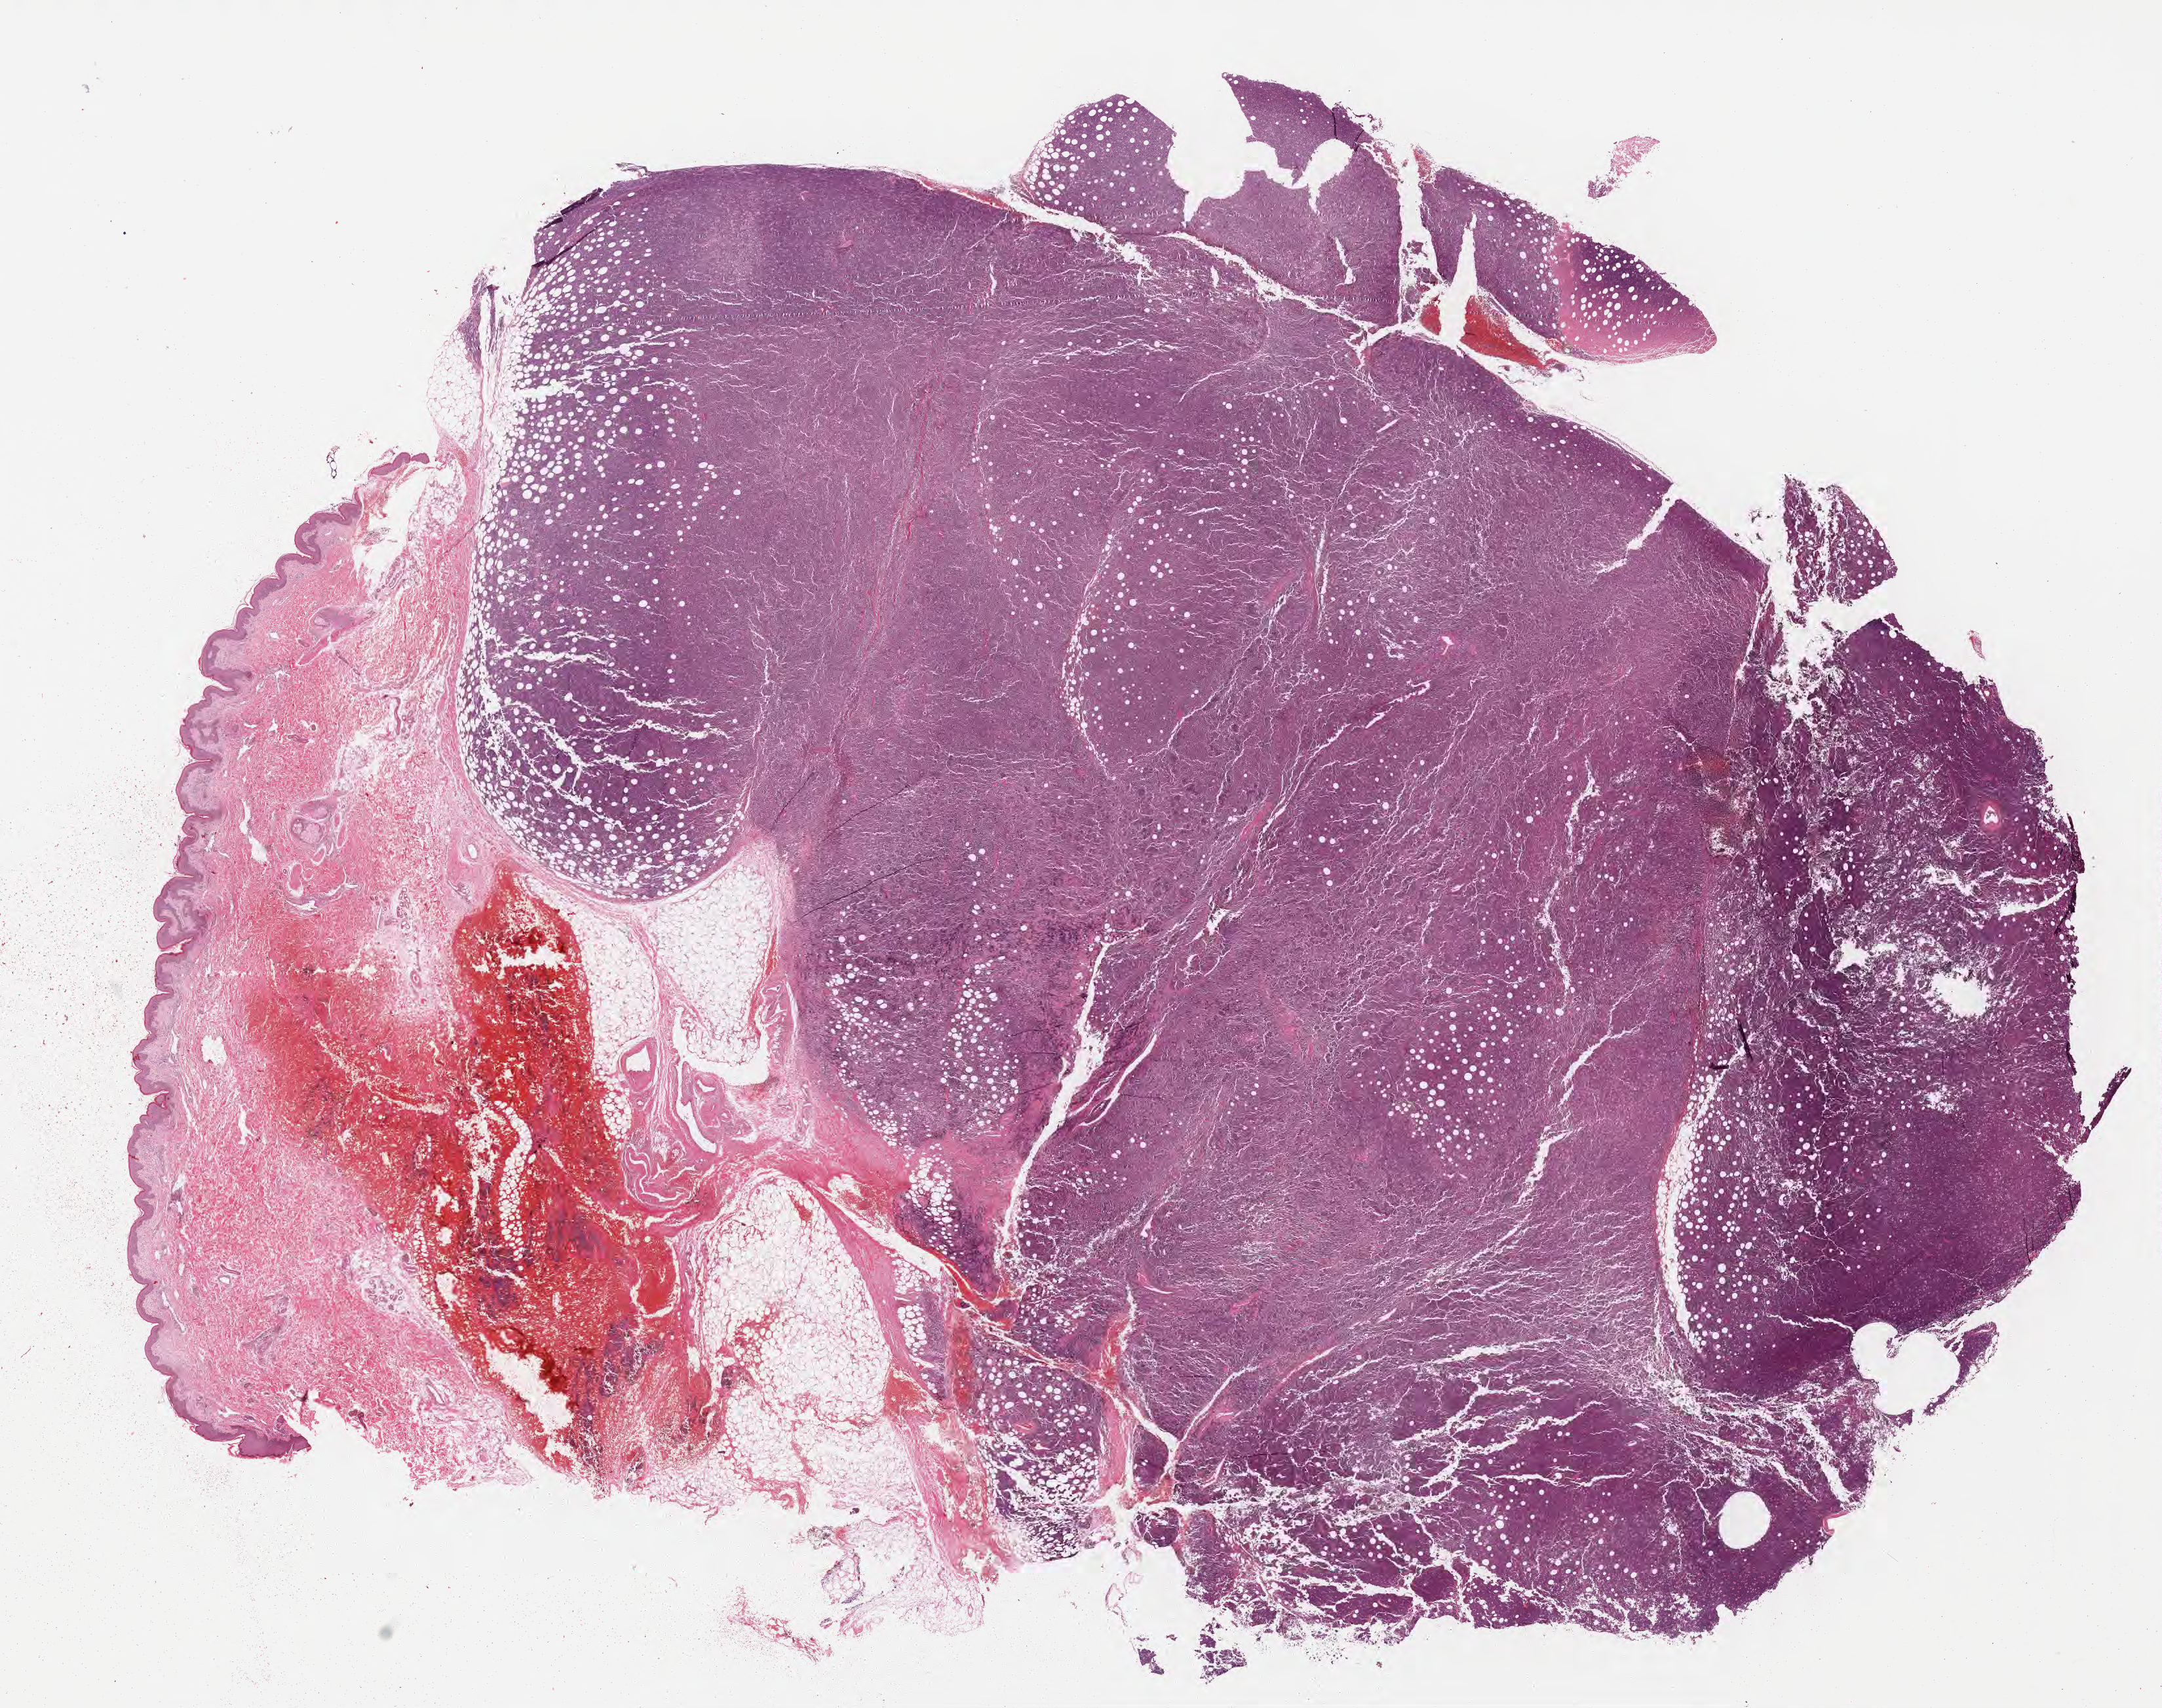
Whole-slide image, hematoxylin and eosin (H&E) stain — whole scanned area (about 26.7 x 21.1 mm) shown as a low-resolution overview, formalin-fixed, paraffin-embedded (FFPE) tissue, specimen: primary tumor. Patient: male, 52 years old. Pathologist review of this section (percent, as recorded): tumor cells 70%, tumor nuclei 95%, stromal cells 0%, necrosis 5%, normal cells 25%. Infiltration values recorded for this section: lymphocyte infiltration 70%, monocyte infiltration 15%, neutrophil infiltration 0%.
* Ann Arbor stage (patient): Stage IV
* section: top of the tissue portion
* histologic diagnosis: Burkitt lymphoma, NOS